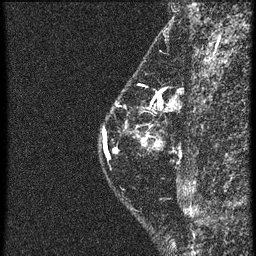
Breast MRI (dynamic contrast-enhanced), one sagittal slice; slice 17 of 60 in the series (ordered by position); 4 images stored at this slice position (order not interpretable as contrast timing); 1.5 T; TE 4.2 ms, TR 20.4 ms; 1.5 mm slice thickness; 256 × 256 image matrix. Female patient, age 46 years. Case-level facts recorded for this patient, not image findings: setting: breast cancer imaged before/during neoadjuvant chemotherapy; receptor status: triple-negative.
Structures marked on this image (semi-automatically segmented with operator editing):
- analysis volume of interest (the breast-tissue region the enhancement analysis was run in; not a lesion): box from (x=98, y=82) to (x=163, y=183) px
- tumour enhancement mask (voxels above the 90 % enhancement threshold inside the analysis volume of interest): (x=104, y=134)–(x=117, y=153)